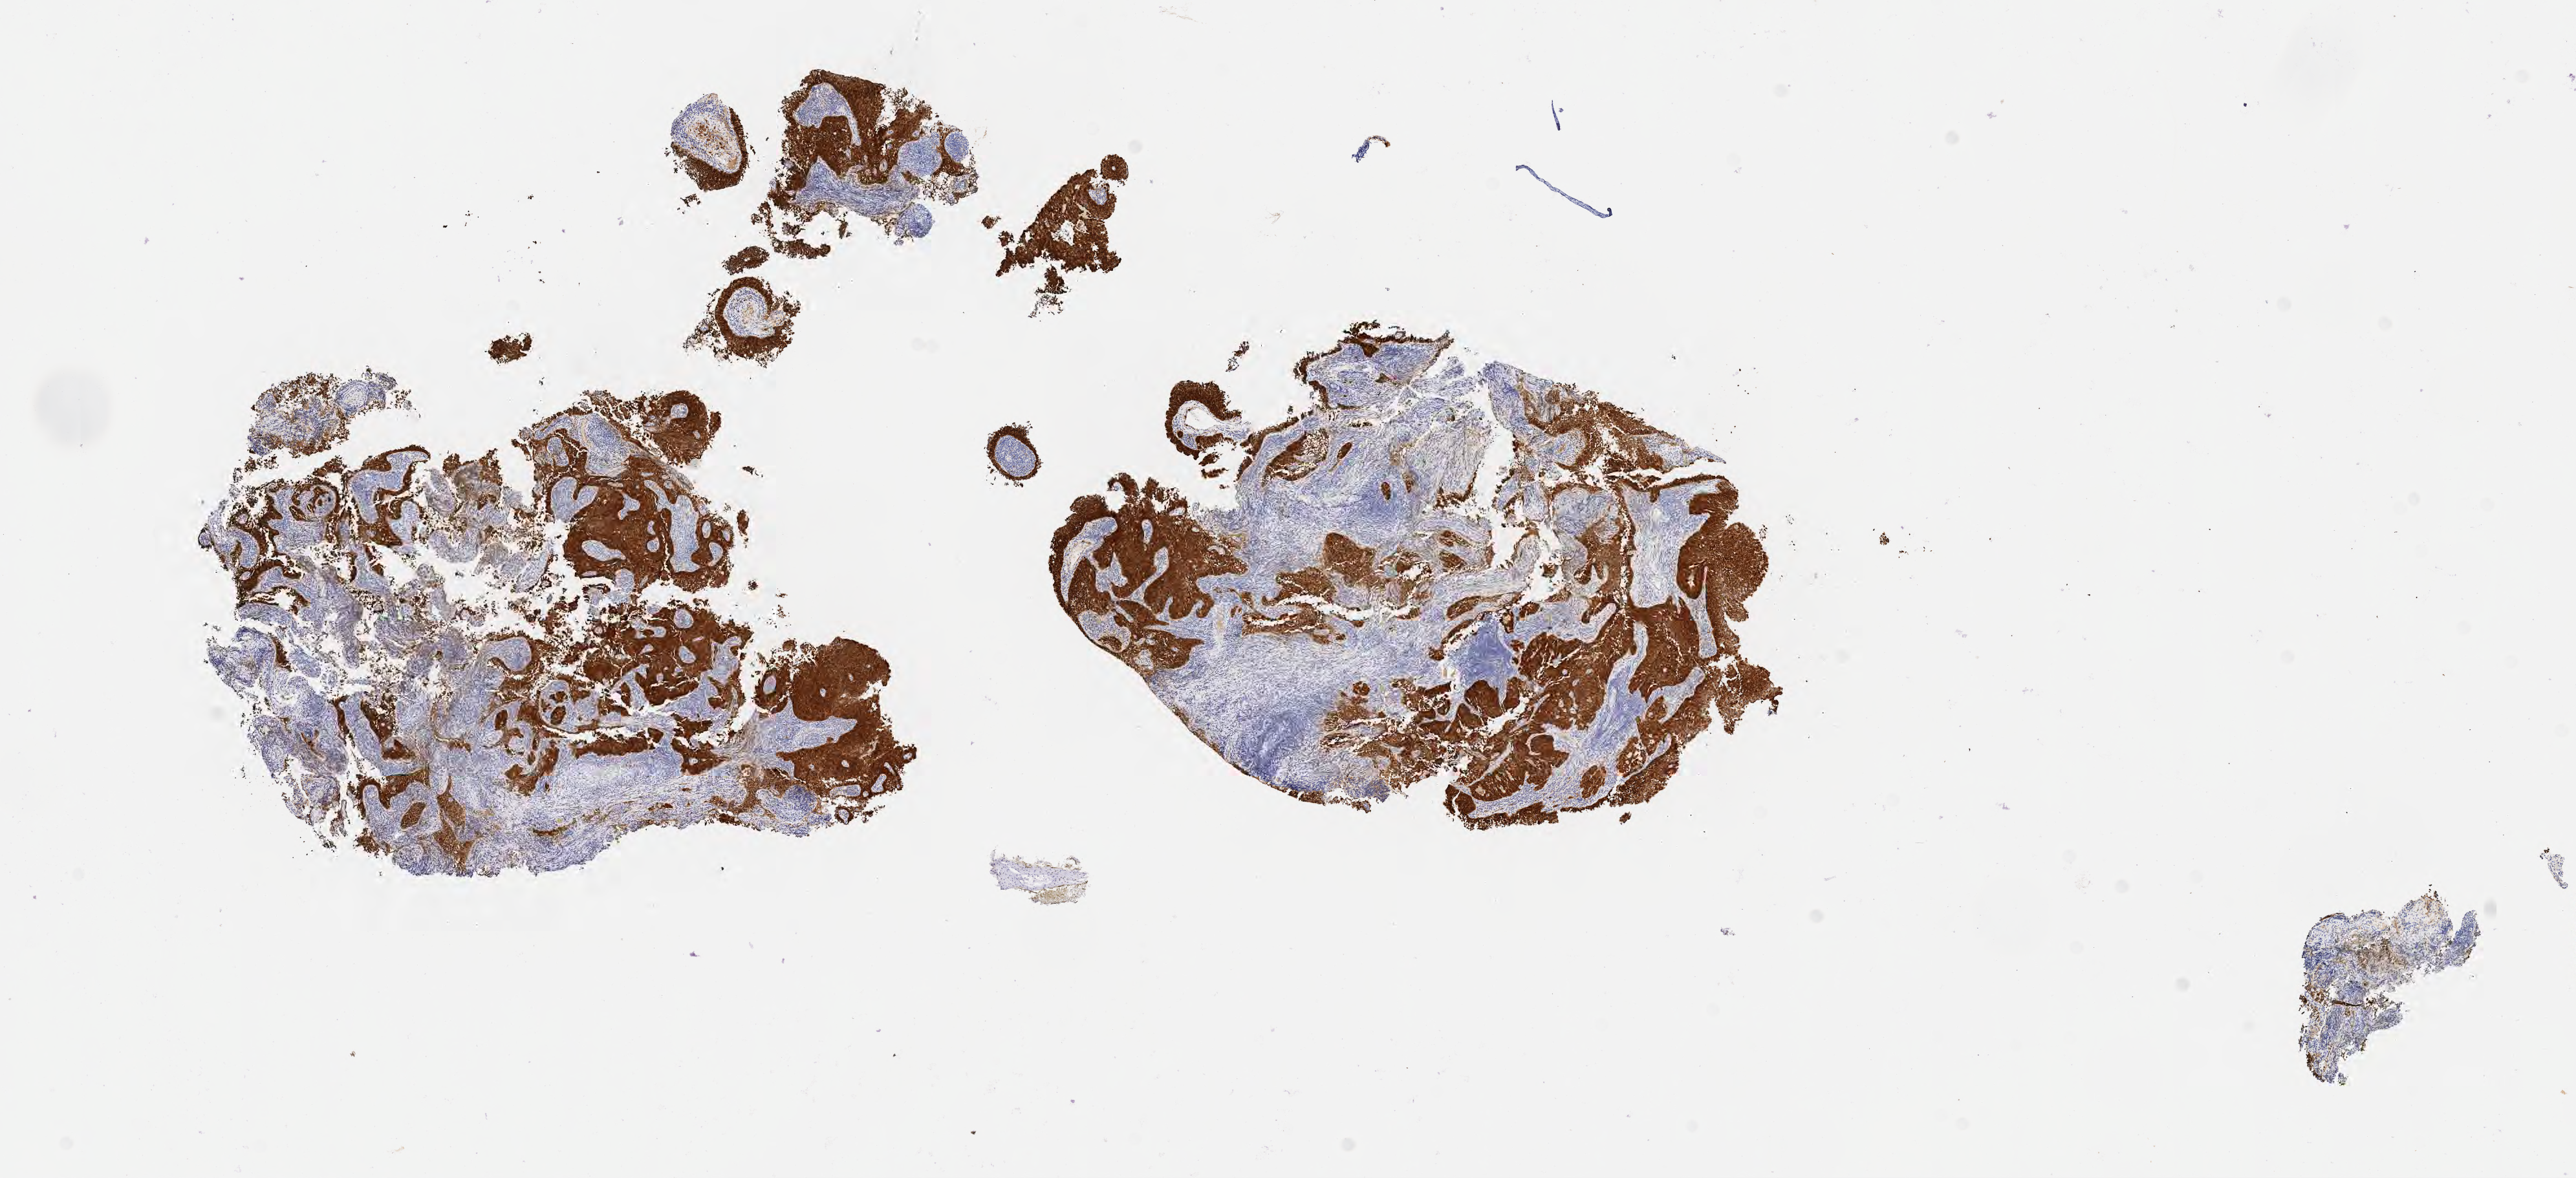
IHC for p16 (p16INK4a), whole-slide image, a low-resolution overview of the entire scanned area, about 16.1 x 7.4 mm; specimen: tumor tissue; anatomic site: cervix. Female patient, age 65 years.
• diagnosis: Squamous cell carcinoma, large cell, nonkeratinizing, NOS